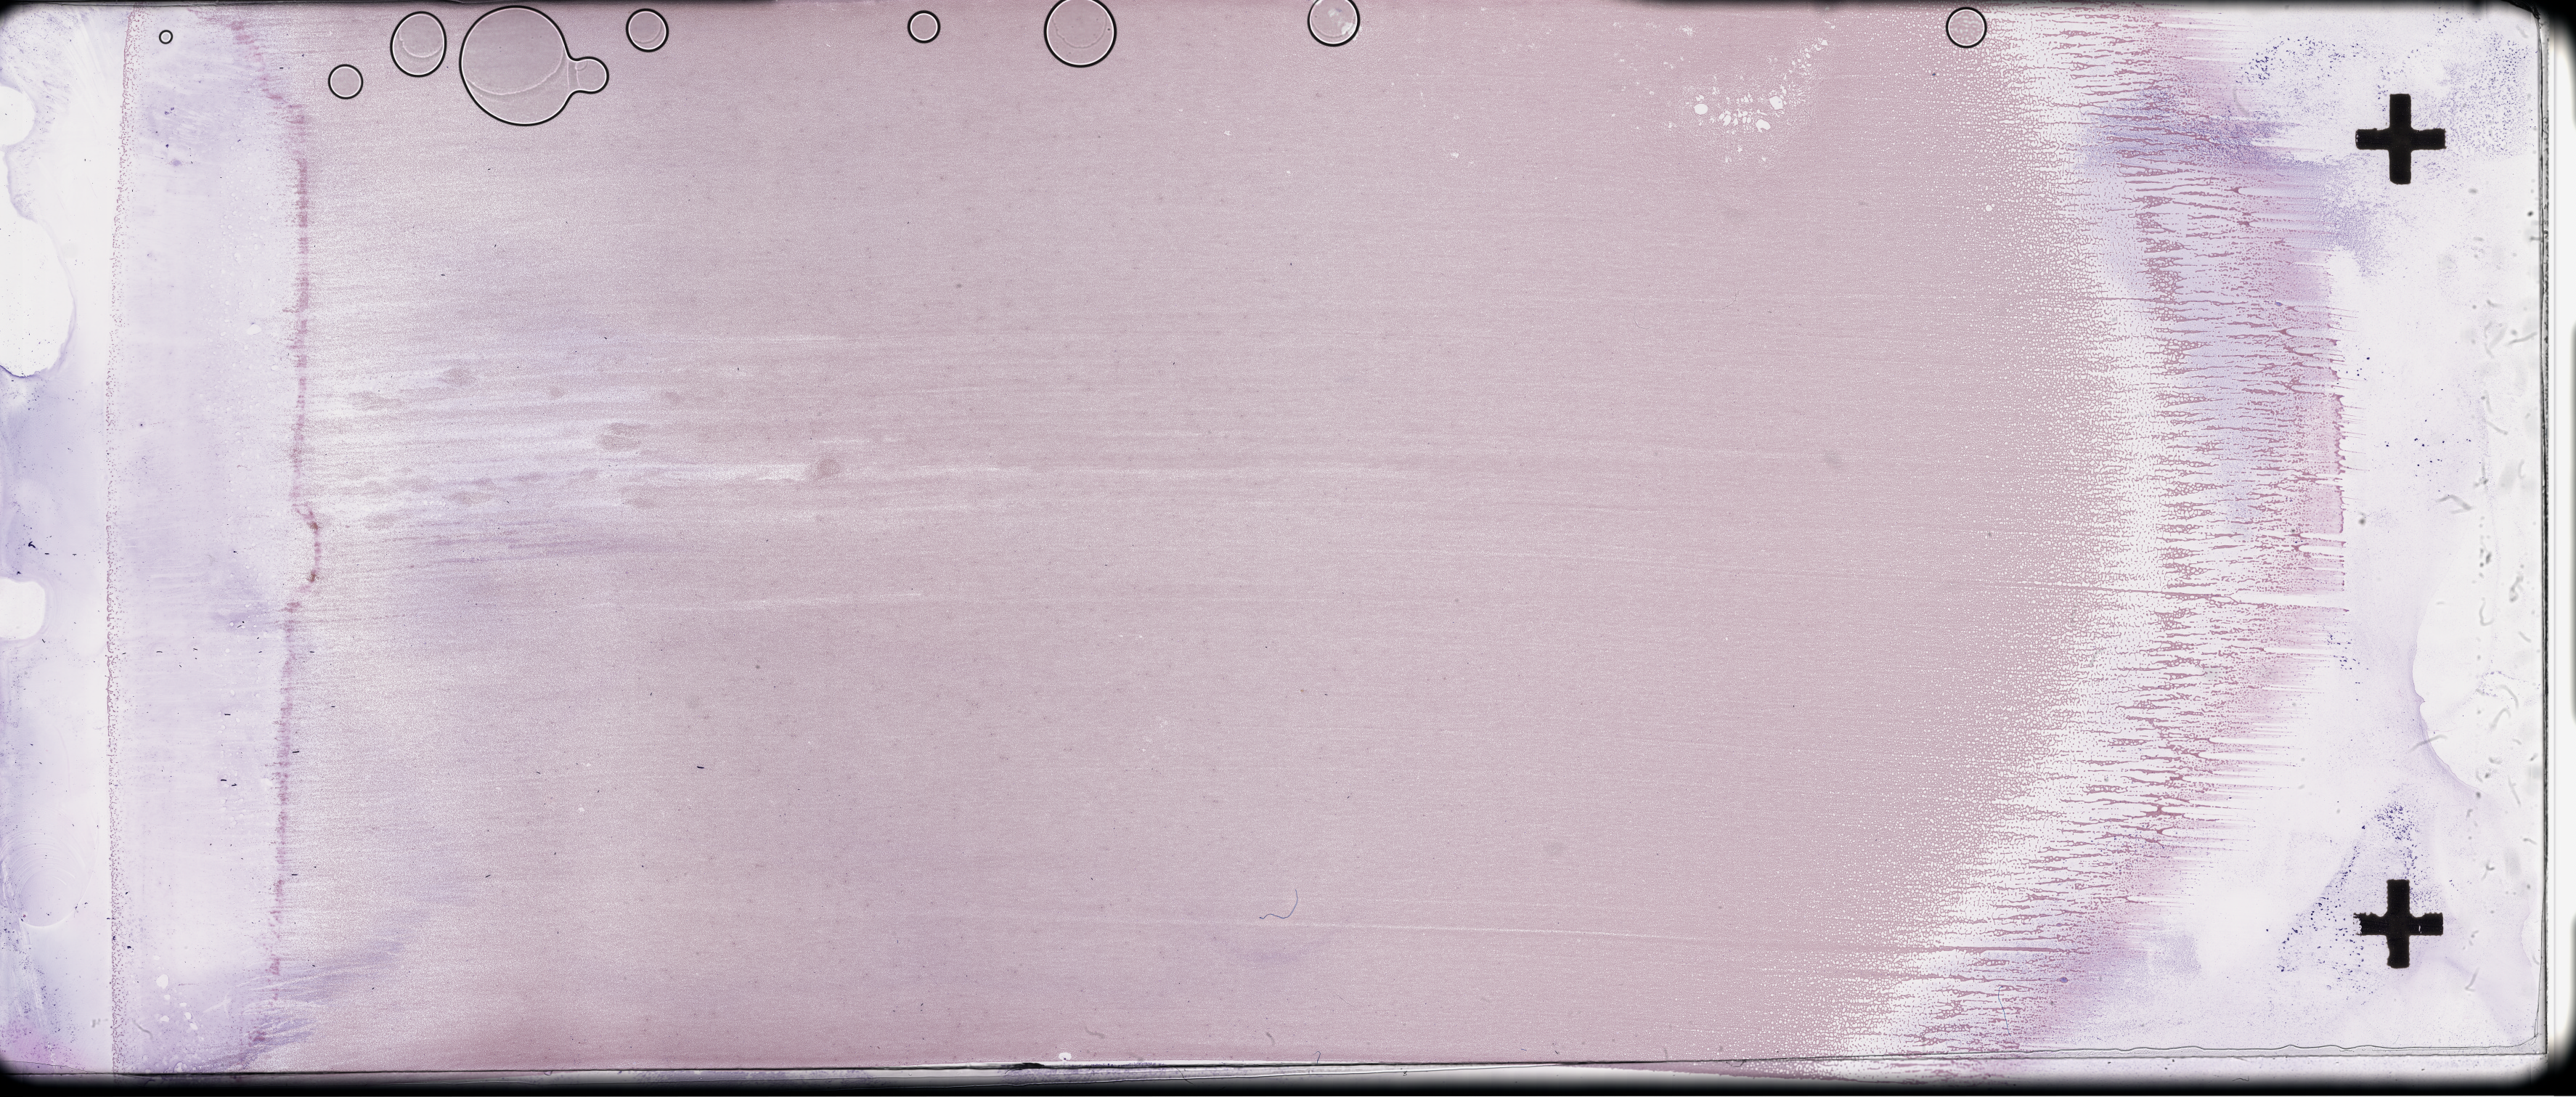
Wright–Giemsa-stained whole blood smear, whole-slide image — a low-resolution overview of the entire scanned area, about 57.3 x 24.4 mm; EDTA-anticoagulated smear. Patient: male.
From a patient with: Plasma Cell Myeloma.